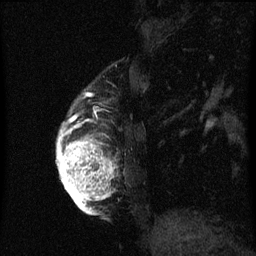
Breast MRI (dynamic contrast-enhanced), one sagittal slice; position 12 of 60 along the scan axis; dynamic contrast-enhanced series, image 2 of 3 at this slice position (ordered by acquisition); 1.5 T; TE 4.2 ms, TR 8 ms; 2 mm slice thickness; 256 × 256 image matrix. Patient: female, 56 years.
Outlined on this slice (semi-automatically segmented with operator editing):
- analysis volume of interest (the breast-tissue region the enhancement analysis was run in; not a lesion): bounding box (x1, y1, x2, y2) in pixels: (58, 98, 119, 219)
- tumour enhancement mask (voxels above the 70 % enhancement threshold inside the analysis volume of interest): (58, 126, 115, 215)